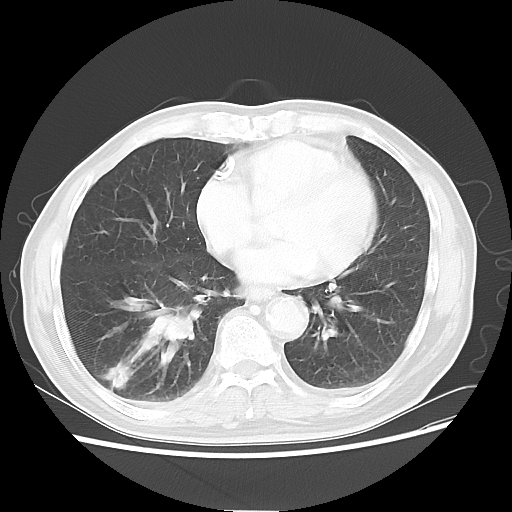
Chest CT, one axial slice. Position 22 of 58 along the scan axis. Reconstruction kernel LUNG. Lung window (W 1500 / L -600 HU). 5 mm slice thickness. 512 × 512 image matrix, field of view 360 × 360 mm. Male patient, age 74 years. From the clinical record (not read from this slice): clinical TNM (as recorded): T1c N1 M1.
Outlined on this slice (bounding box drawn by a radiologist):
- lung tumour (recorded histology: adenocarcinoma): bounding box <128,293,198,364> (left, top, right, bottom; pixels)